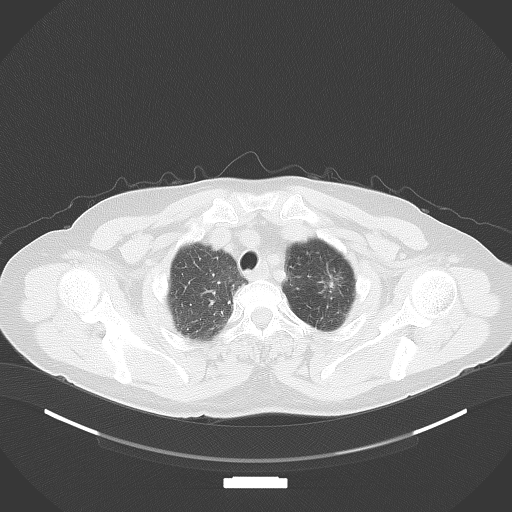
Chest CT, one axial slice; position 74 of 116 along the scan axis; reconstruction kernel B70f; 120 kVp; lung window (W 1500 / L -600 HU); 3 mm slice thickness; 512 × 512 image matrix. Patient: female, 64 years. Case-level facts recorded for this patient, not image findings: clinical TNM (as recorded): T1c N0 M0; histopathological grade: G1.
Outlined on this slice (bounding box drawn by a radiologist):
- lung tumour (recorded histology: adenocarcinoma): bounding box [x1, y1, x2, y2] px = [326, 274, 337, 297]